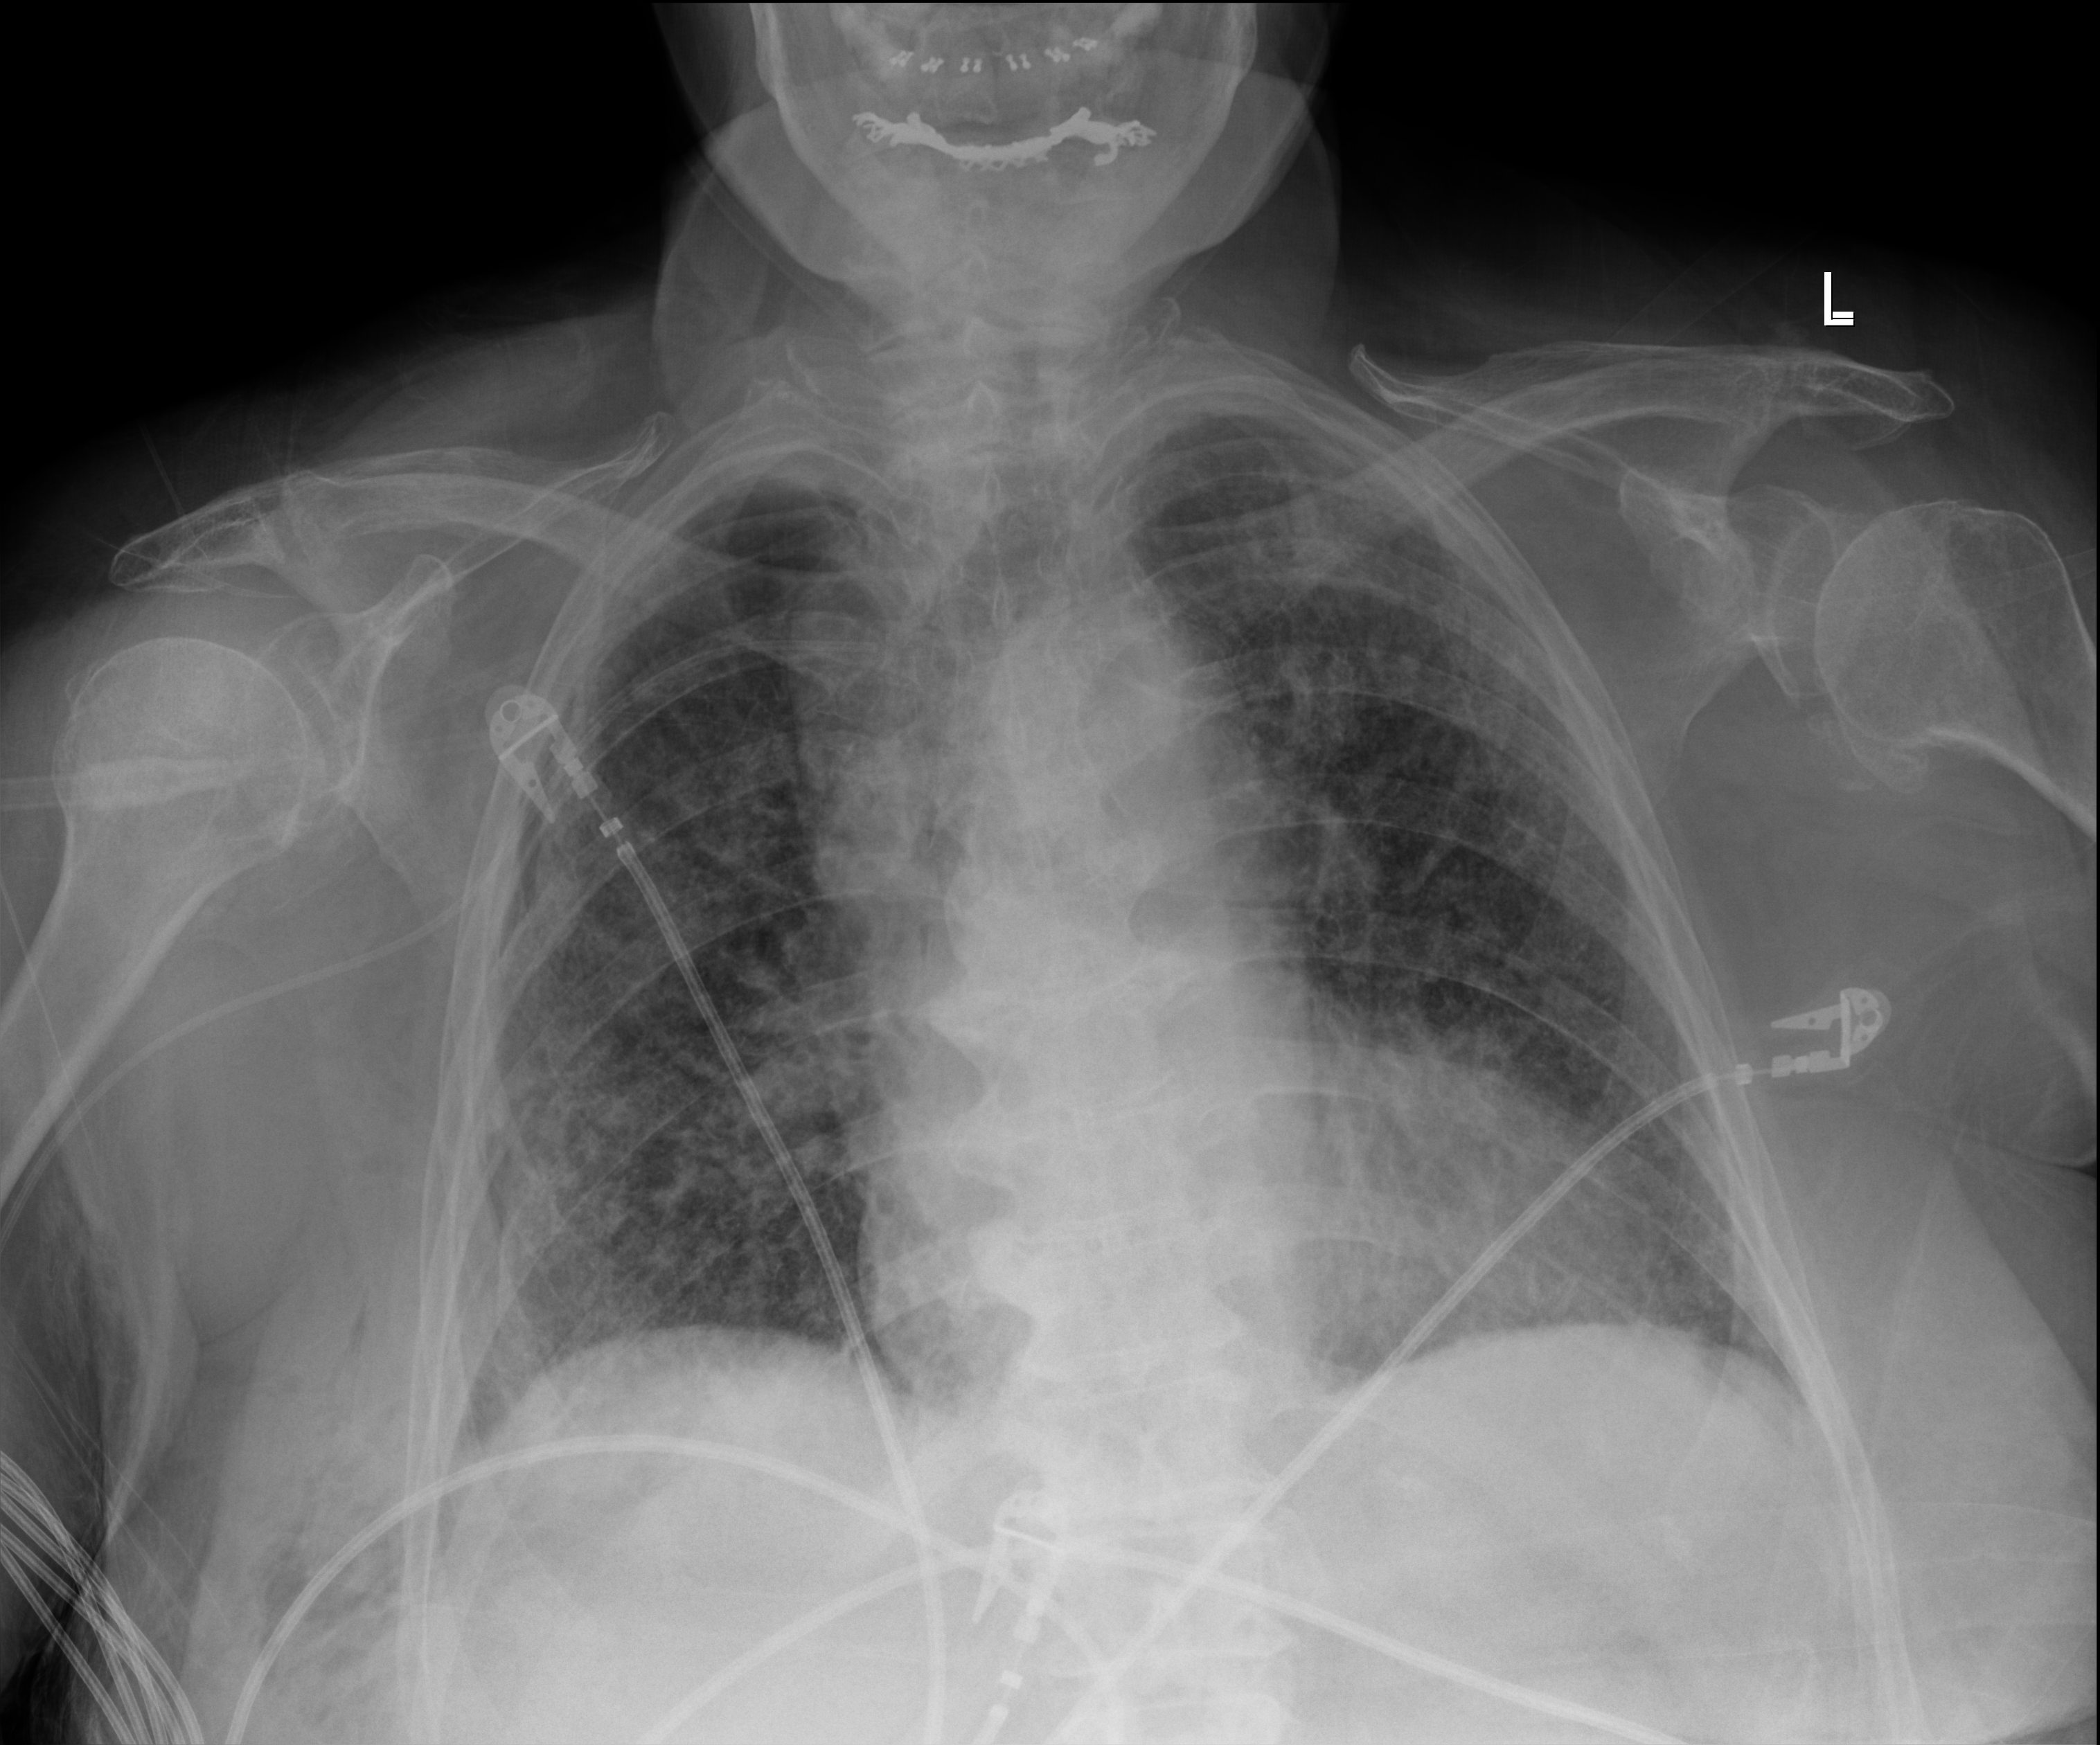
Bedside chest radiograph (digital radiography), anteroposterior (AP) projection. Patient hospitalised with COVID-19; female, aged 75–90 years.
Hospital-stay facts (about this admission, not read from this image; timing relative to this image not recorded): hypertension (admission record): no; mechanically ventilated during this hospital stay: yes.